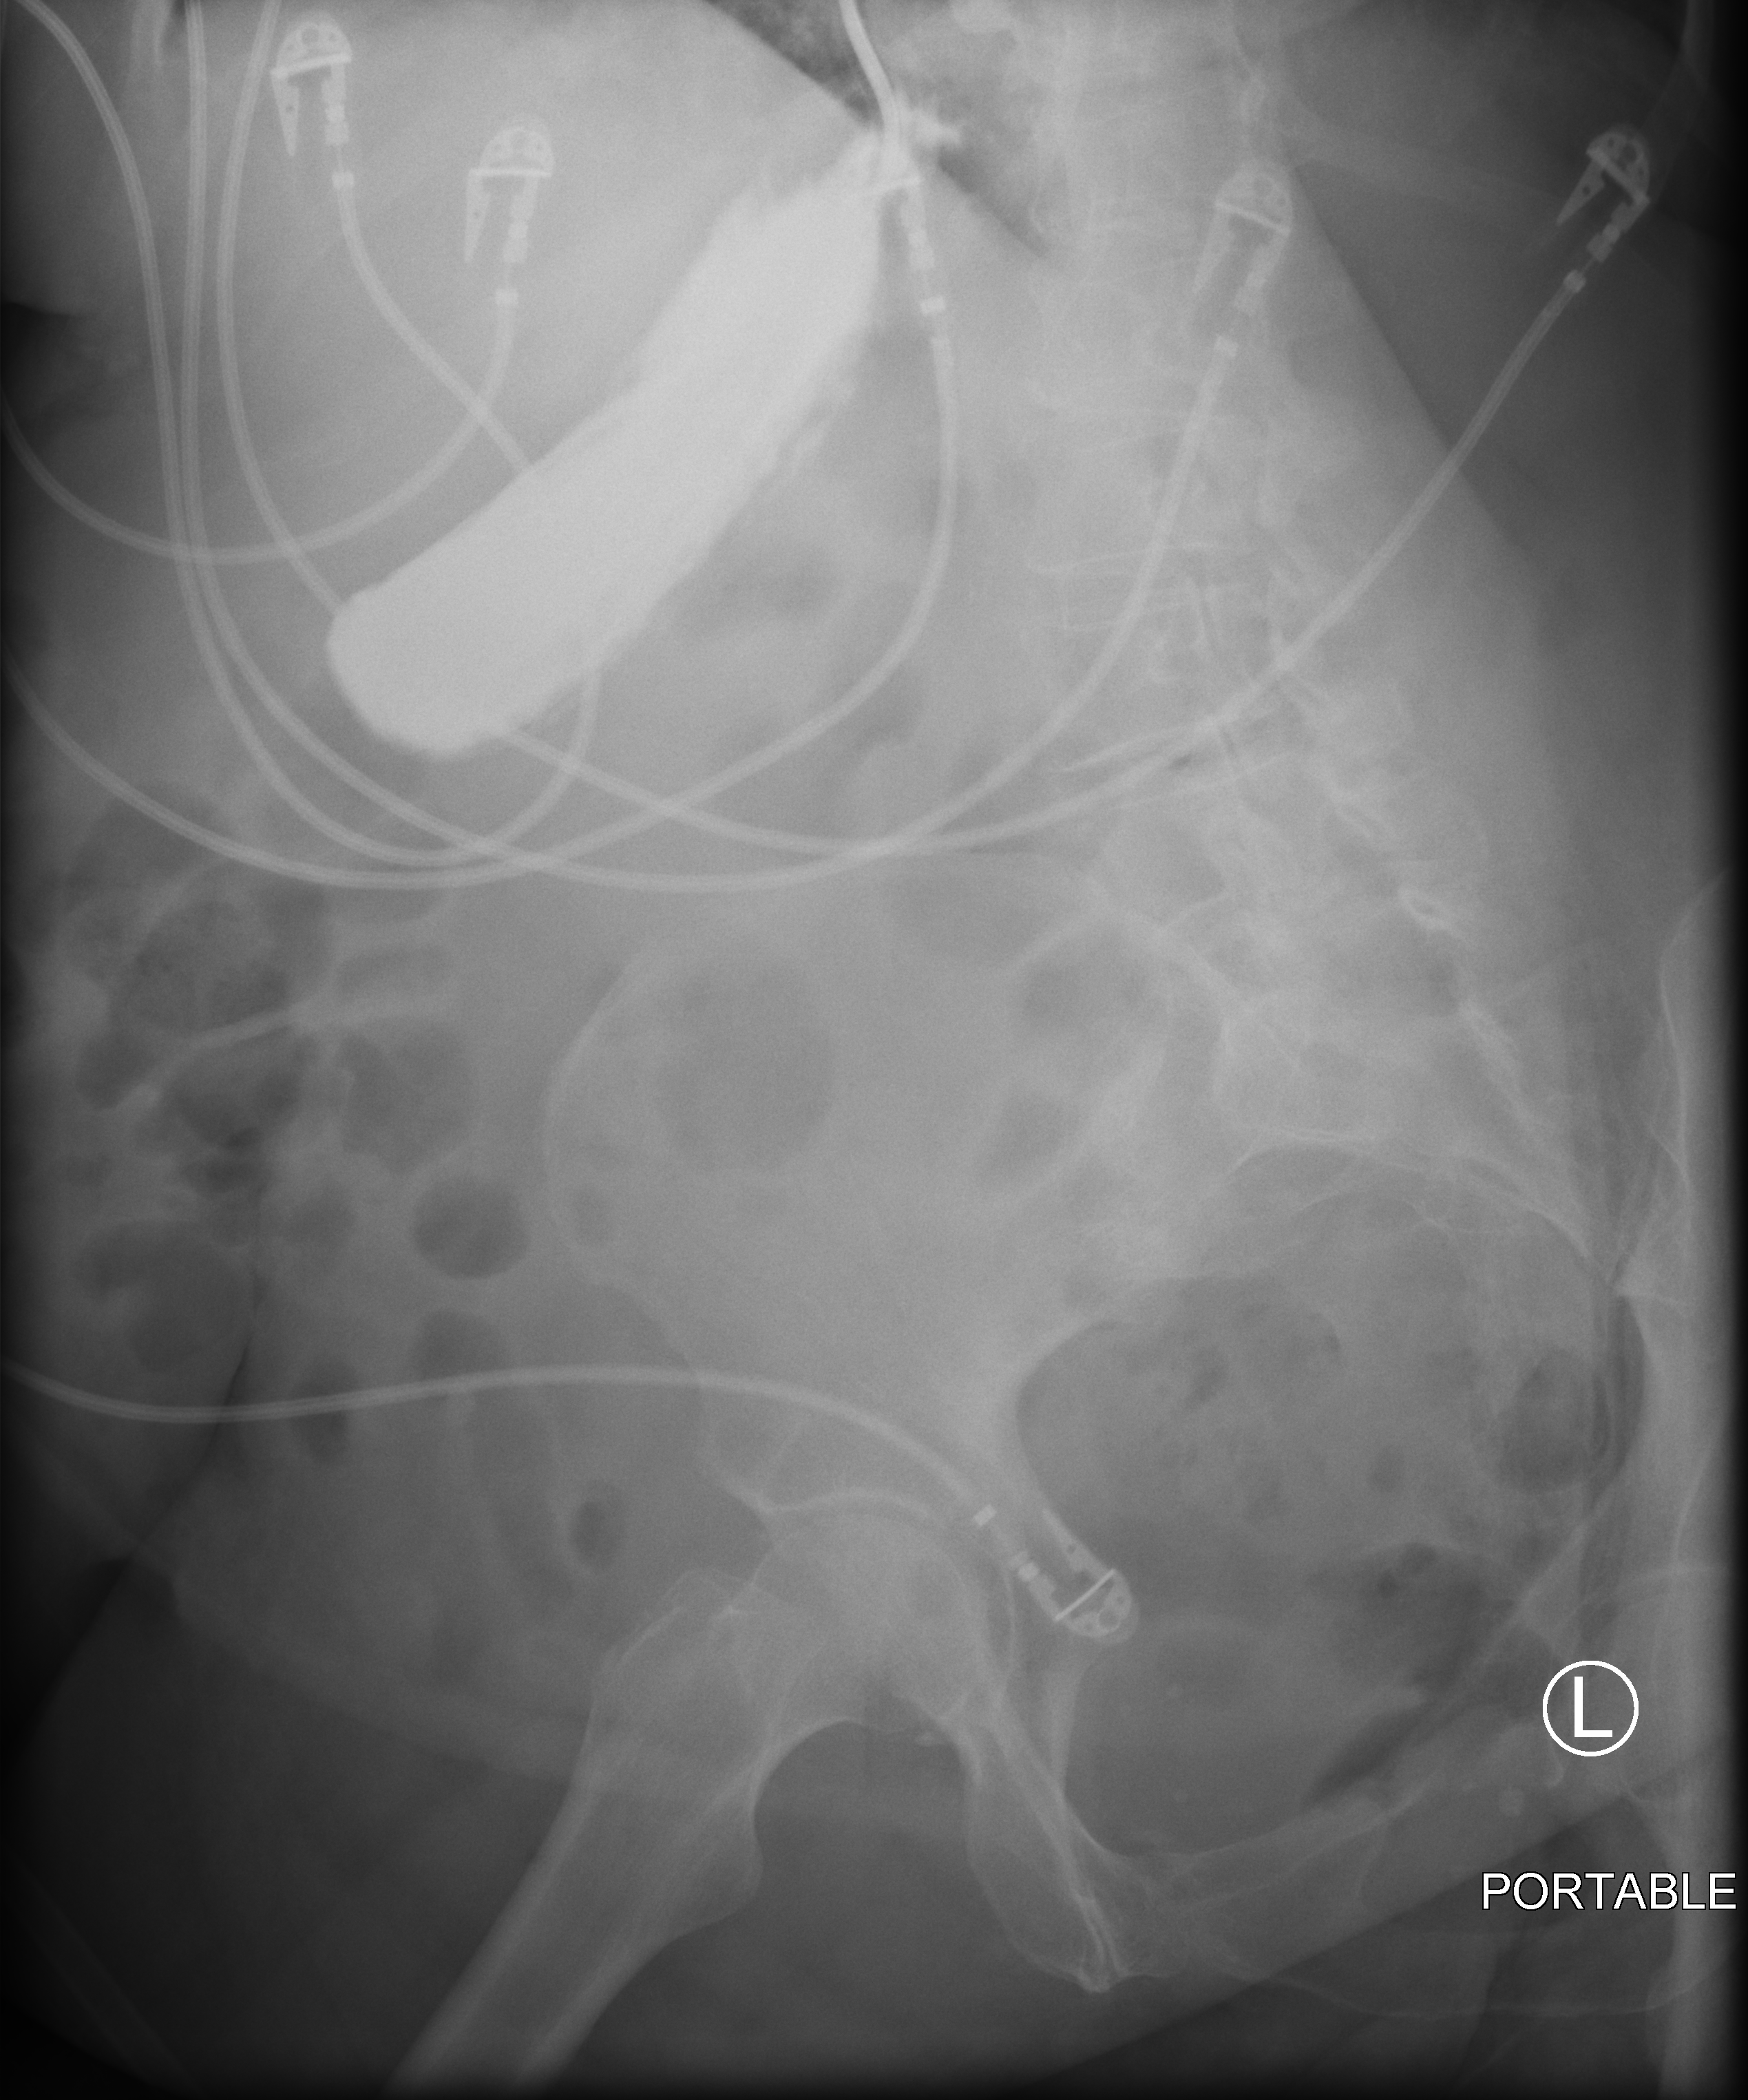
Portable abdomen radiograph; anteroposterior (AP) projection. Female patient hospitalised with COVID-19, age 75–90 years.
Admission-level facts for this patient (not findings on this image; timing relative to this image not recorded): length of hospital stay: 31 days.